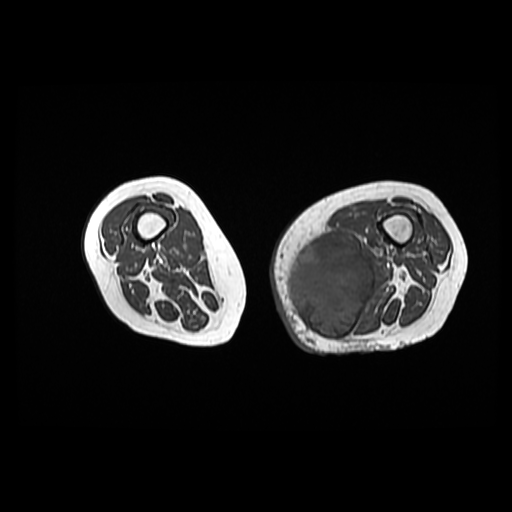
MRI of an extremity soft-tissue mass, one axial slice; position 26 of 42 along the scan axis; 512 × 512 image matrix, field of view 420 × 420 mm. Female patient. From the clinical record (not read from this slice): histological type: pleomorphic leiomyosarcoma; grade: high; site of the primary tumour: left thigh.
Annotated regions visible in this slice (outlined manually by an expert reader):
- gross tumour volume including surrounding oedema: box from (x=288, y=239) to (x=379, y=340) px
- gross tumour volume (mass): (x=288, y=239)–(x=375, y=340)